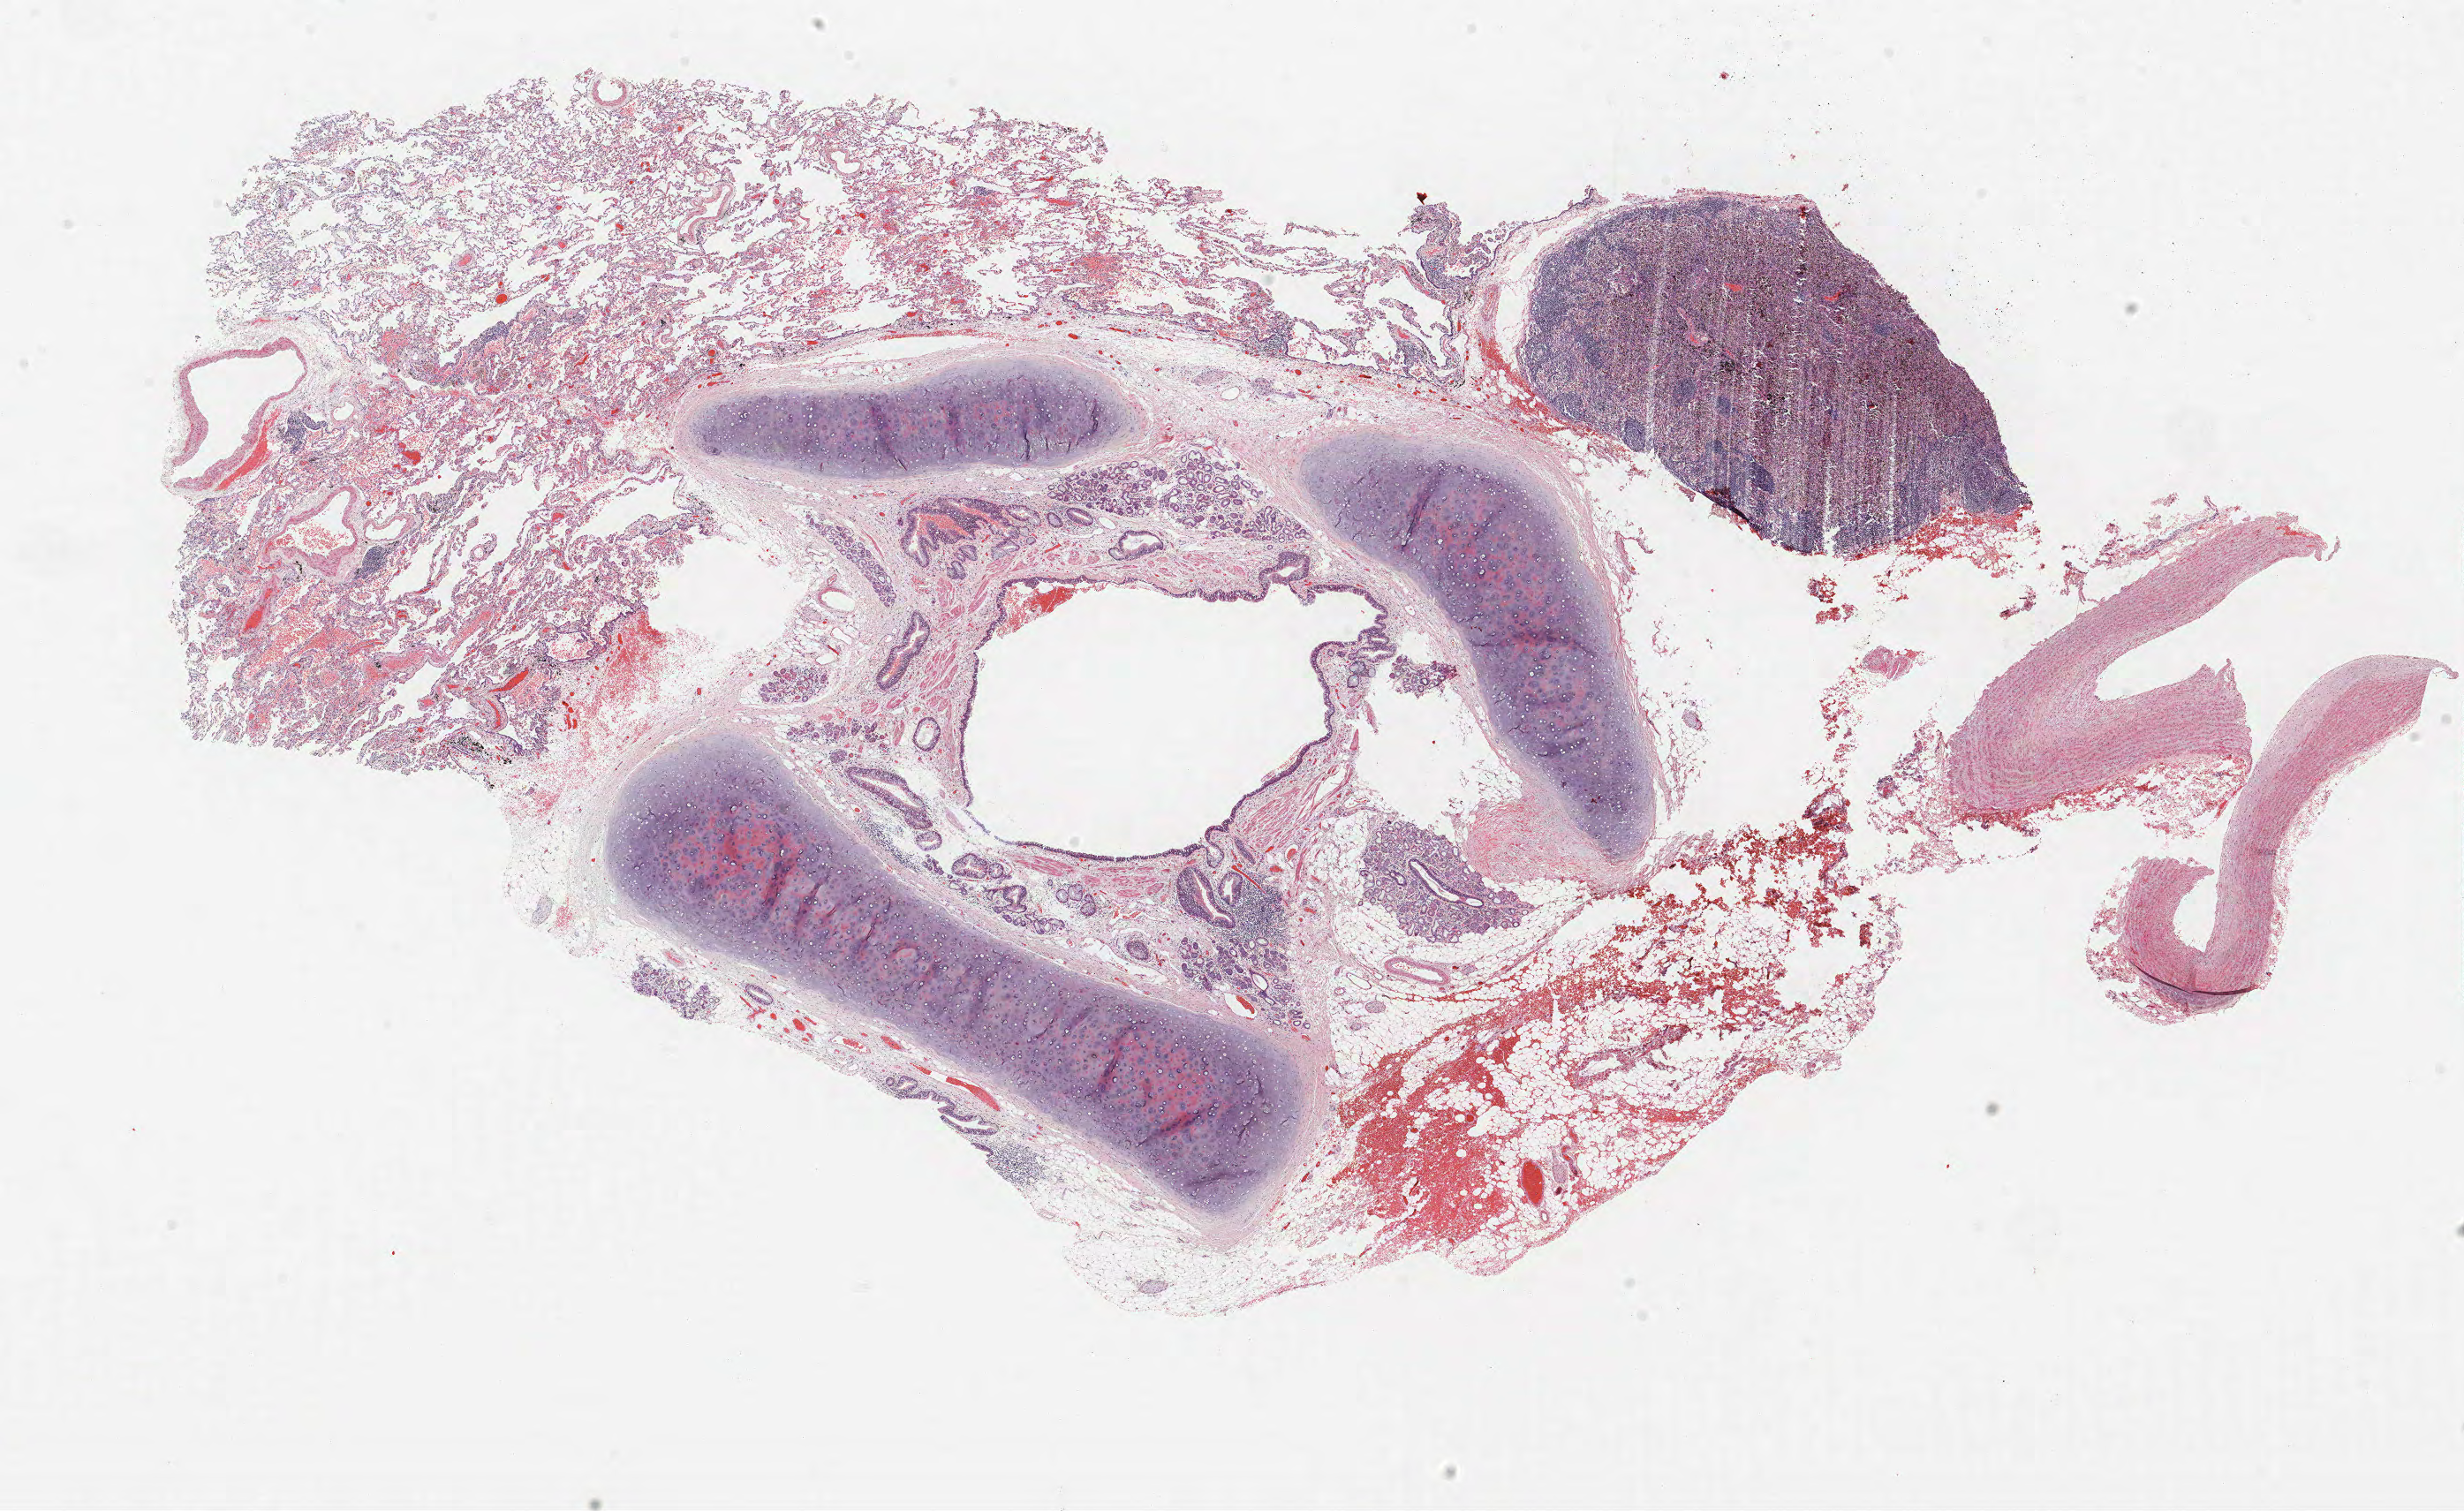
Whole-slide histology image, H&E, low-resolution overview of the scanned area, about 22.3 x 13.7 mm (acquisition: 40x scan), FFPE section, lung. Male patient, aged 64 at enrolment. Grade: moderately differentiated (G2).
Primary tumour location (clinical record): left upper lobe. Participant's lung-cancer diagnosis: Squamous cell carcinoma, NOS (ICD-O-3 8070/3). Stage (AJCC 6th edition): IA. Tumour size (pathology): 10 mm.